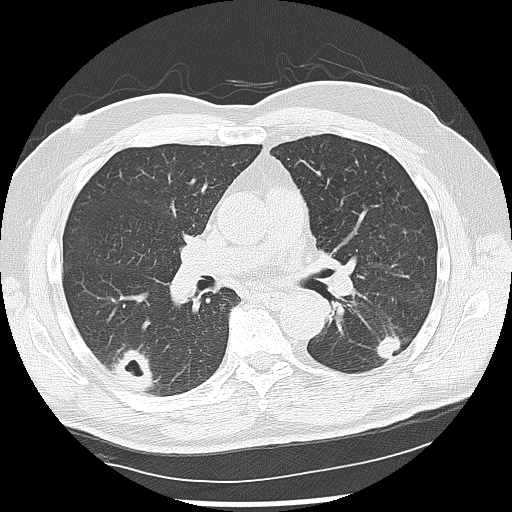
Low-dose screening chest CT, one axial slice. Position 72 of 142 along the scan axis. Reconstruction kernel LUNG. 120 kVp. Lung window (W 1500 / L -600 HU). 2.5 mm slice thickness. 512 × 512 image matrix, field of view 360 × 360 mm.
Structures marked on this image (expert manual segmentation):
- lesion 1 (nodule, lower lobe of left lung): box from (x=376, y=335) to (x=401, y=359) px
- lesion 2 (nodule, lower lobe of right lung): (x=110, y=350)–(x=155, y=391)